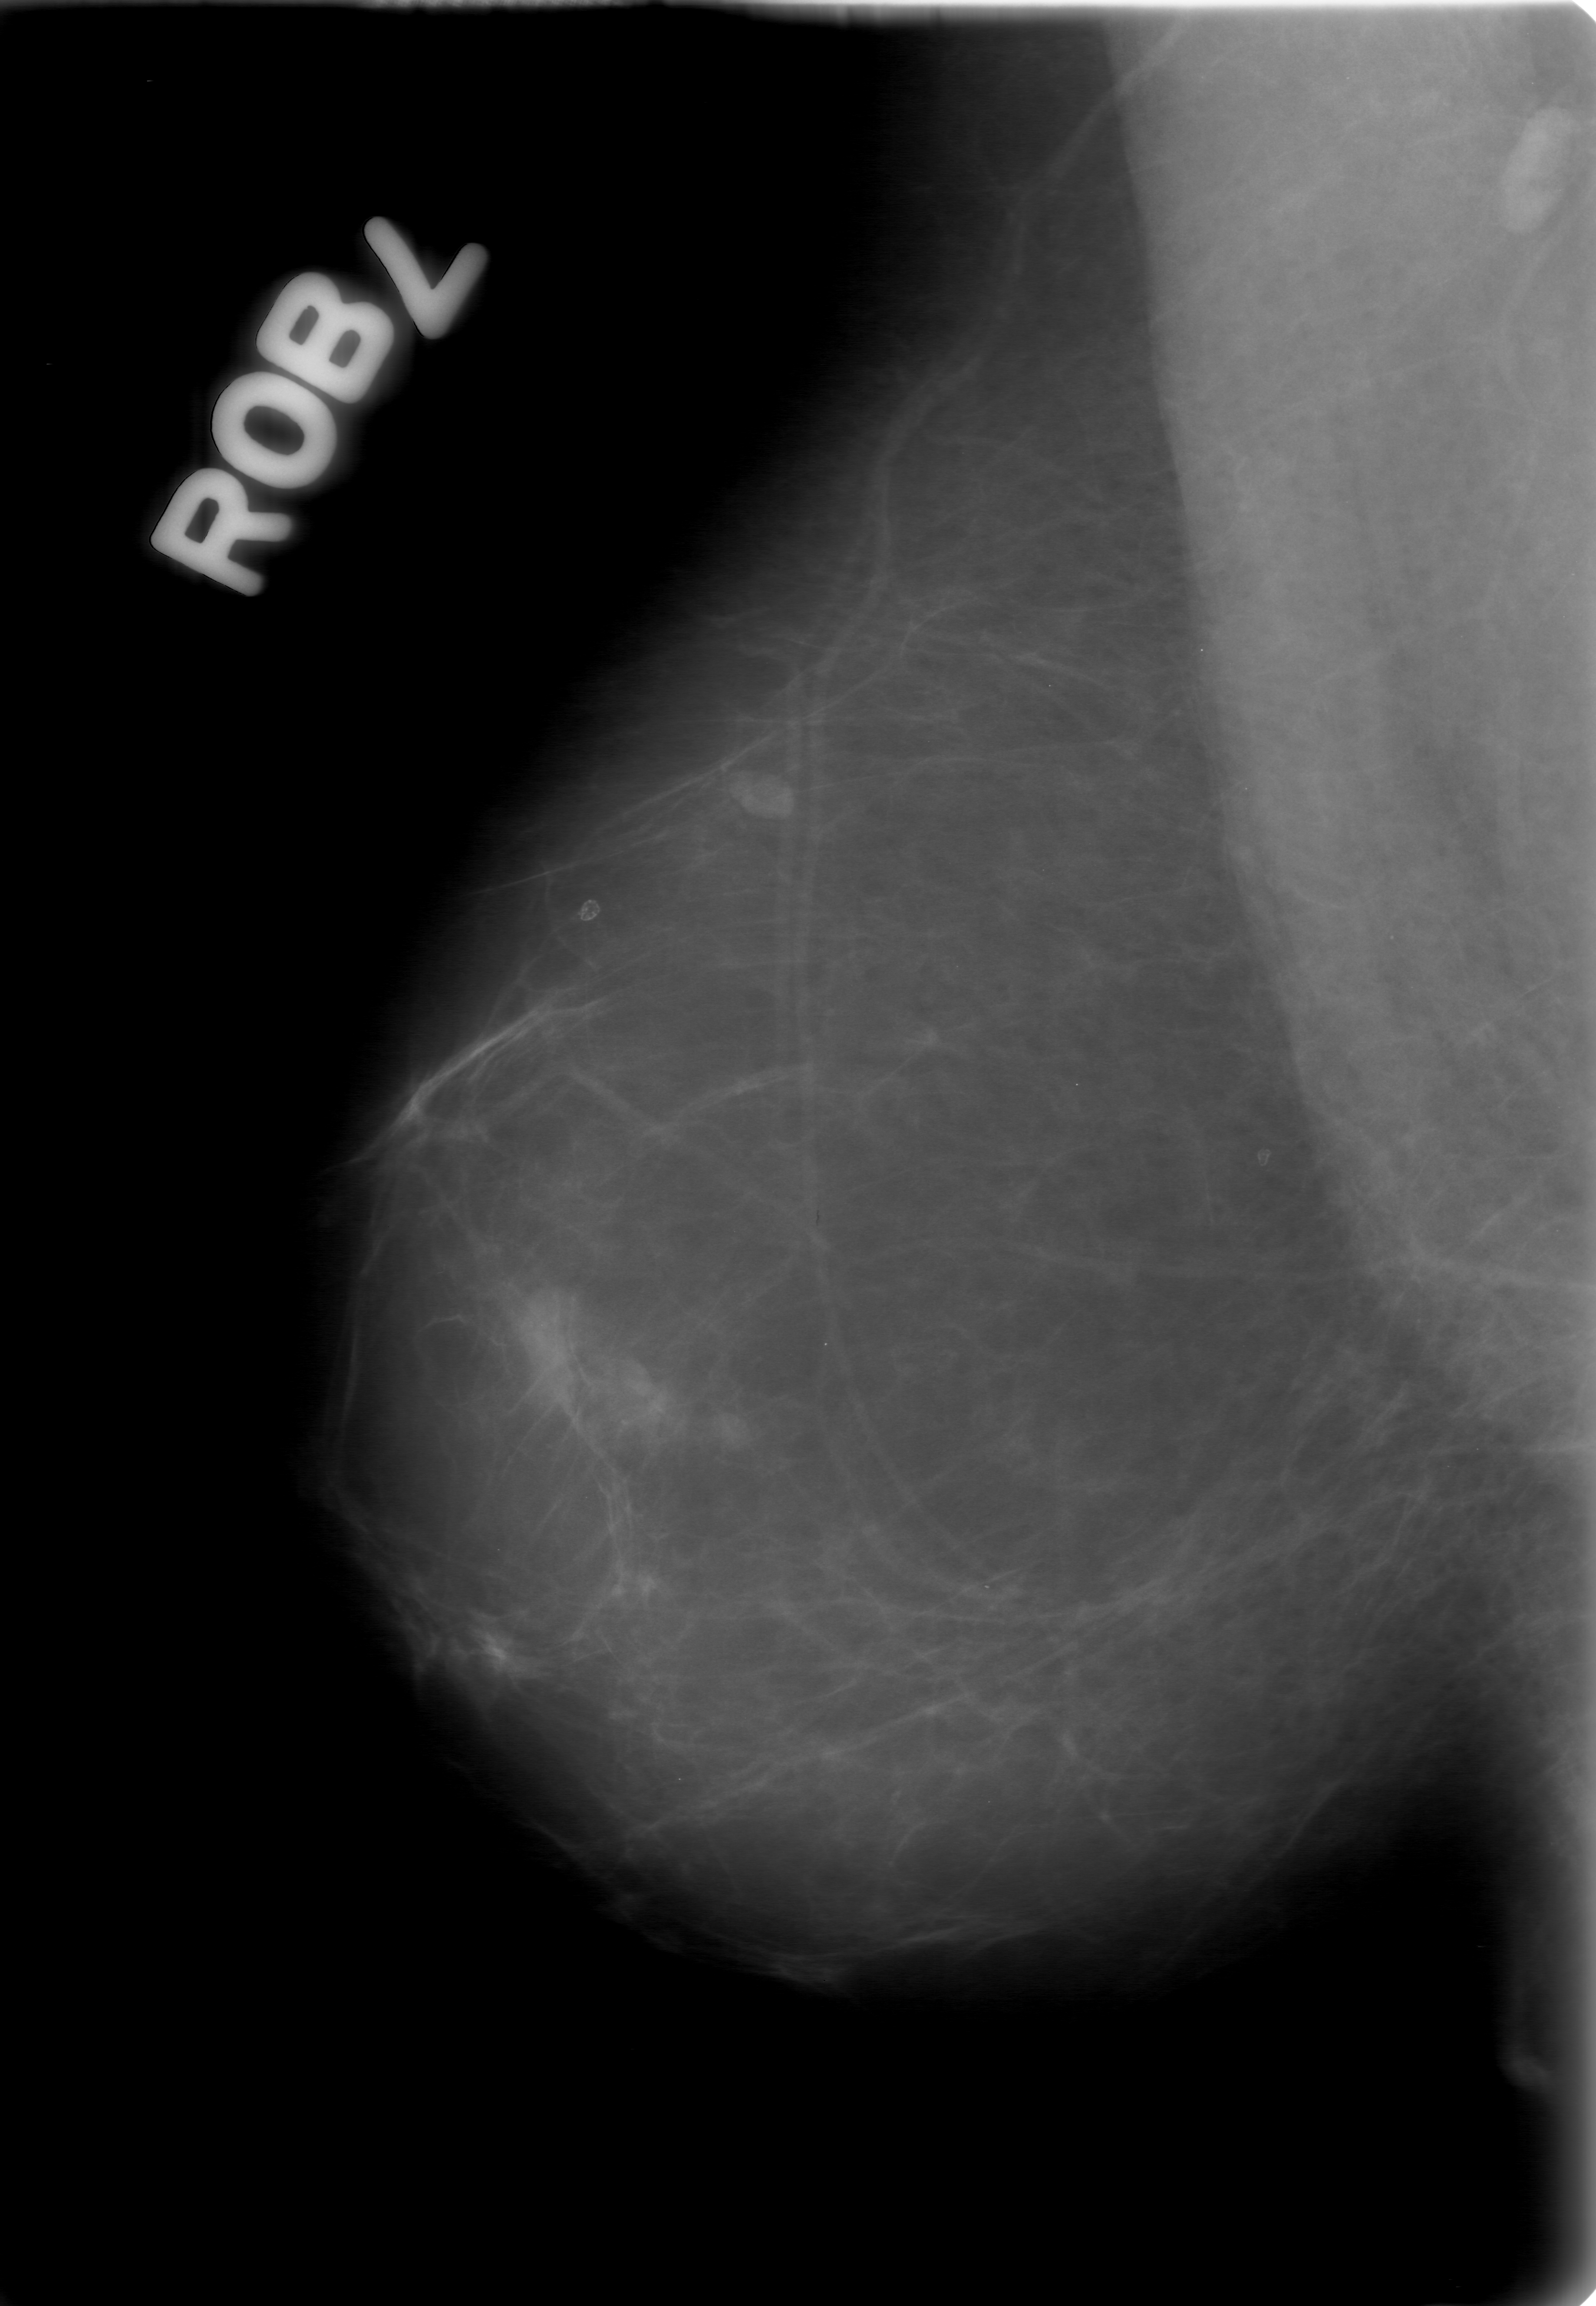
Digitized screen-film mammogram; right breast; MLO view.
Radiologist-marked abnormalities on this image: mass, shape lobulated, margins obscured; BI-RADS assessment category 0; subtlety rating 2 on a 1 (subtle) to 5 (obvious) scale; pathology result (as recorded, not read from the image): benign.